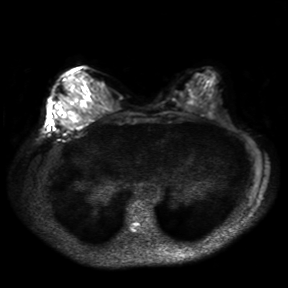
Breast MRI, one axial slice. Position 13 of 30 along the scan axis. Diffusion-weighted series; image 2 of 4 stored at this slice position (different b-values; order by instance number). 3 T. 4 mm slice thickness. 288 × 288 image matrix. Female patient.
Annotated regions visible in this slice (outlined manually by an expert reader):
- tumour on diffusion-weighted imaging: box from (x=65, y=111) to (x=79, y=122) px